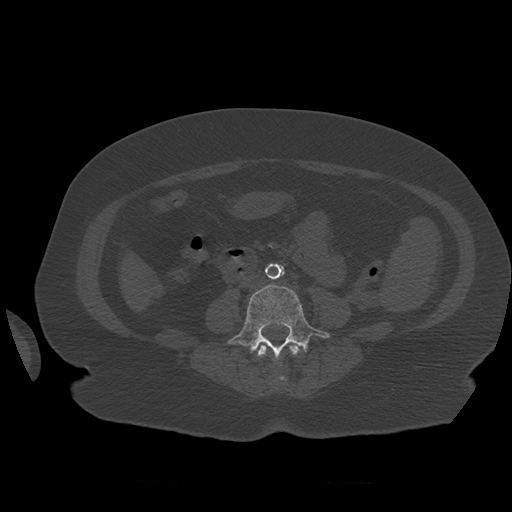
CT including the spine, one axial slice; bone window (W 1800 / L 400 HU); 1.25 mm slice thickness; 512 × 512 image matrix, field of view 404 × 404 mm. Patient age 81 years. Case-level facts recorded for this patient, not image findings: primary cancer: renal; vertebrae with lytic lesions (as recorded): L1.
Structures marked on this image (semi-automatically segmented with operator editing):
- L3 vertebra: bounding box (x1, y1, x2, y2) in pixels: (257, 344, 301, 381)
- L4 vertebra: (228, 285, 330, 364)